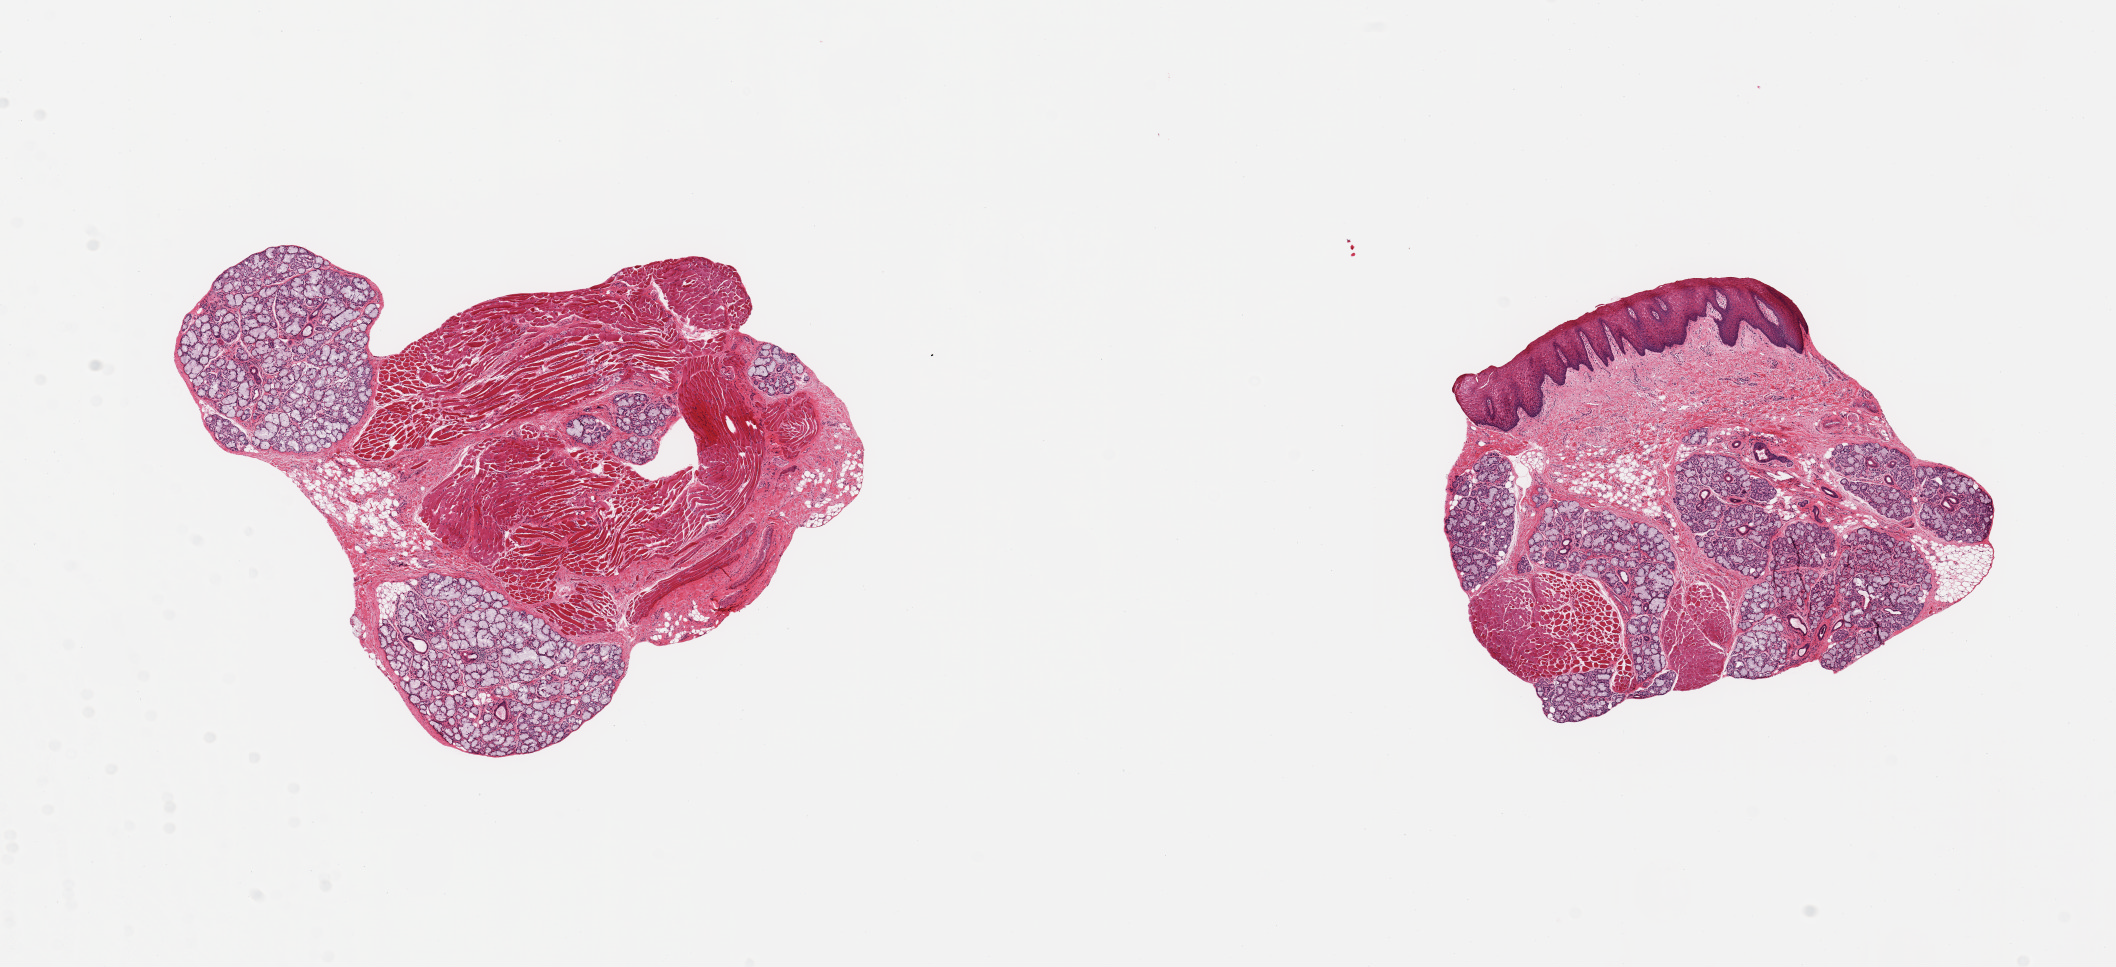
Digitized hematoxylin and eosin (H&E)-stained section, shown as a low-resolution overview of the whole scanned area (about 16.7 x 7.6 mm); PAXgene-fixed, paraffin-embedded tissue; target tissue: minor salivary gland; tissue donor sample. Donor sex: male.
- pathologist's review note for this sample: 2 pieces, ~50% glandular parenchyma (dispersed aggregates); rest is skeletal muscle/stroma/squamous mucosa